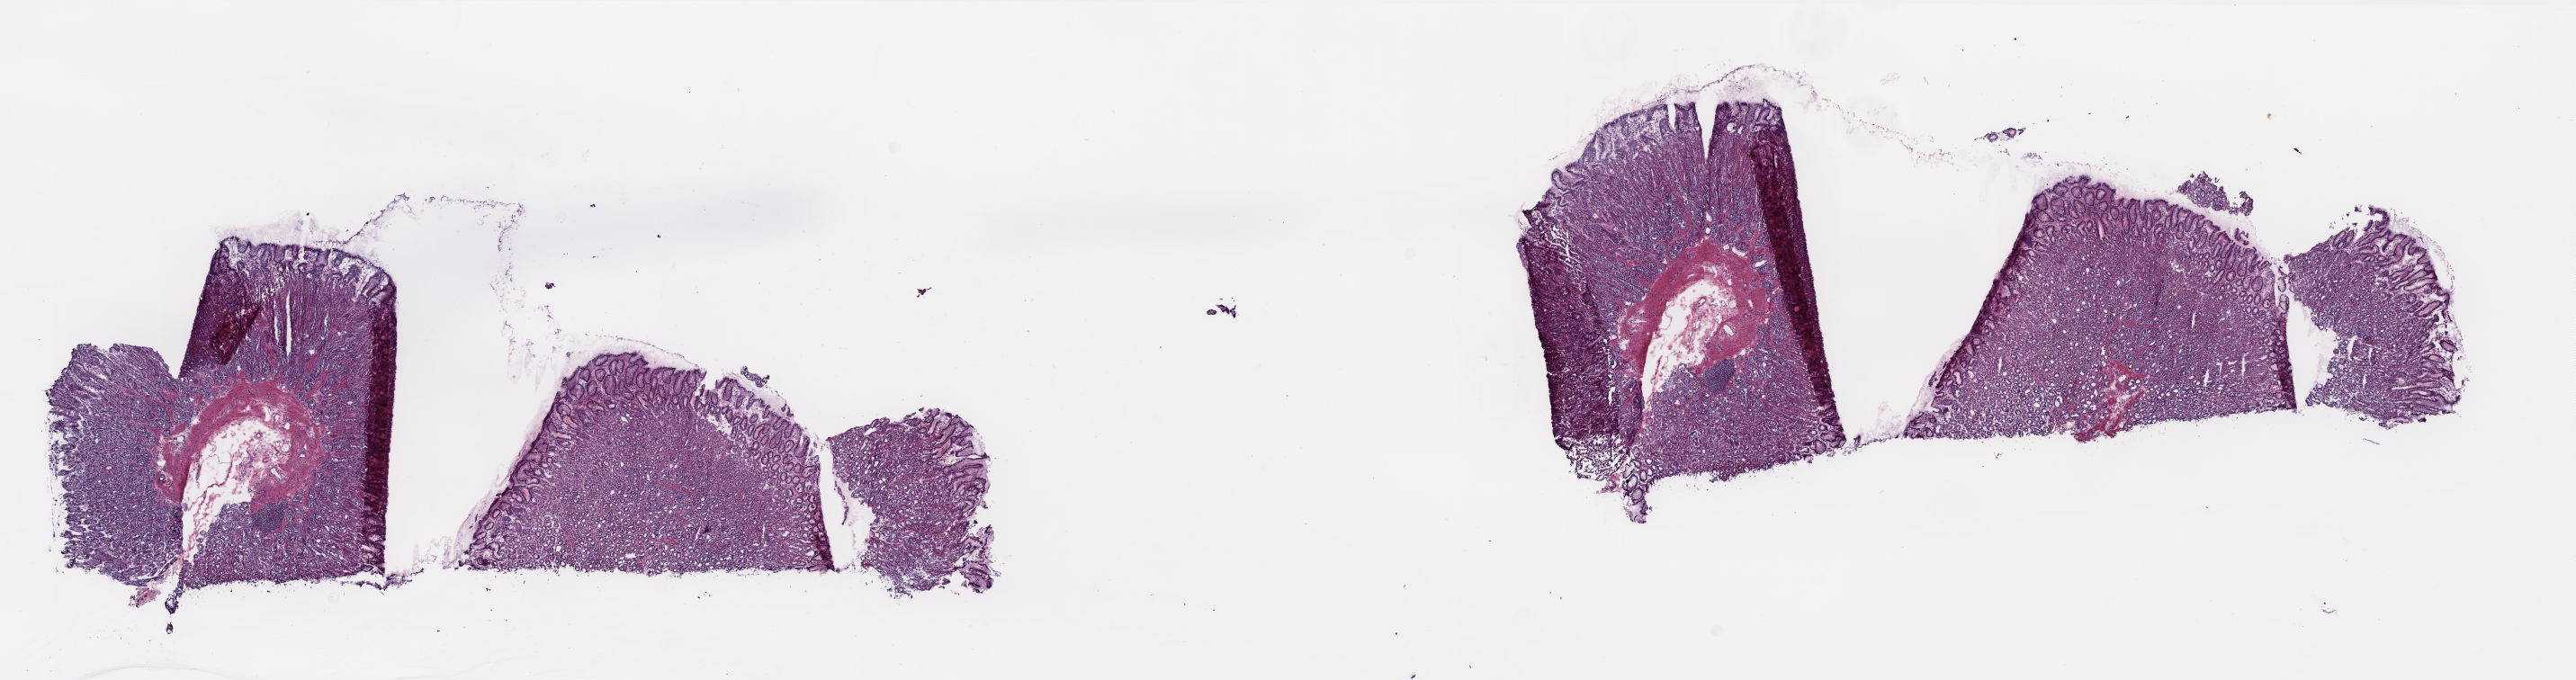
Digitized H&E-stained tissue section (whole slide), low-resolution overview of the scanned area, about 23.1 x 6.1 mm (acquisition: 20x scan), frozen section from the top of the tissue portion, stomach, solid tissue normal (non-tumour tissue) sample. Male, age 70 years at initial diagnosis. Pathologist review of this section (percent, as recorded): tumour cells 0%, tumour nuclei 0%, normal cells 100%, stromal cells 0%, necrosis 0%. Infiltration values recorded for this section: lymphocyte infiltration 0%, monocyte infiltration 0%, neutrophil infiltration 0%.
* this section: solid tissue normal (non-tumour) sample from the same patient
* patient diagnosis: Adenocarcinoma, intestinal type (gastric antrum)